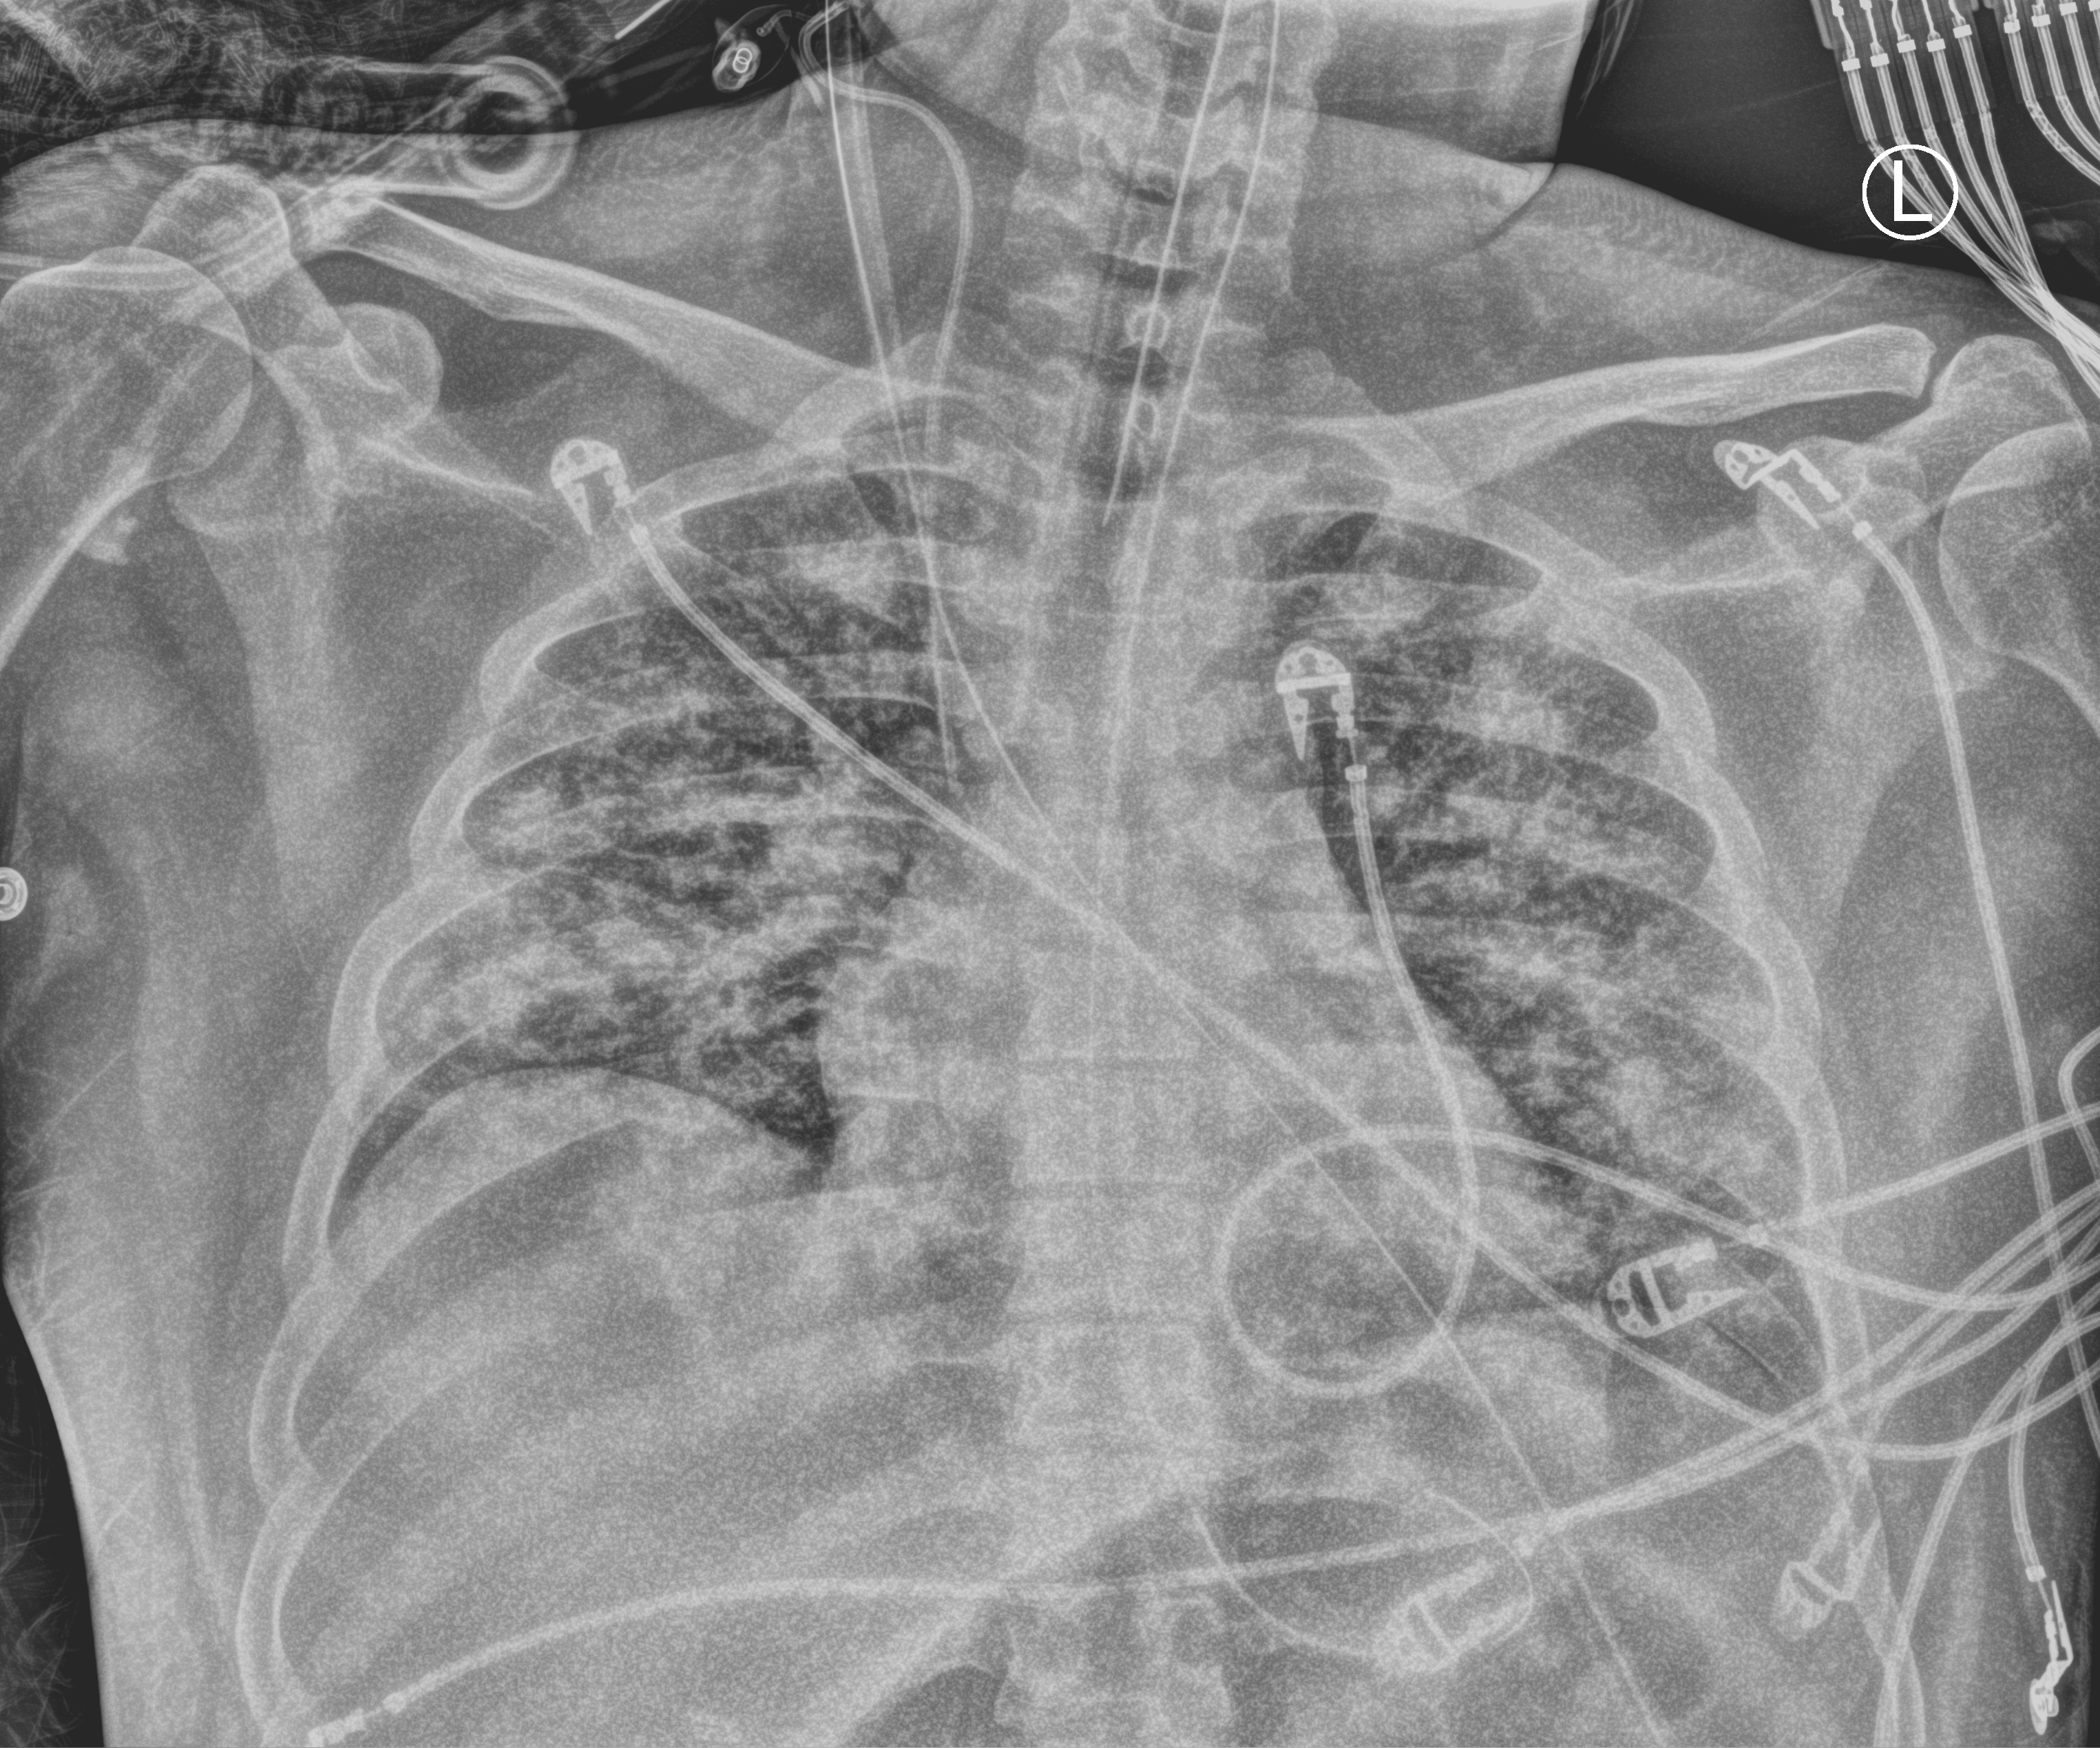
Portable chest radiograph, anteroposterior (AP) projection. Male patient hospitalised with COVID-19, age 18–59 years.
From the hospital-stay record, not from the radiograph (when in the stay this image was taken is not recorded): COPD (admission record): no; smoking status (admission record): former; mechanically ventilated during this hospital stay: yes.